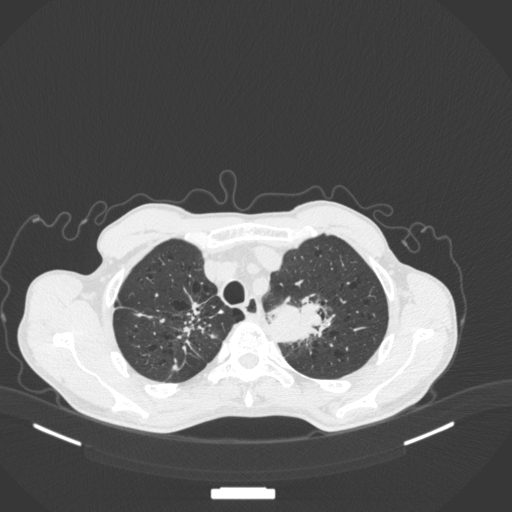
Chest CT, one axial slice; position 355 of 394 along the scan axis; 120 kVp; lung window (W 1500 / L -600 HU); 512 × 512 image matrix, field of view 400 × 400 mm. Patient: male, 65 years. Case-level facts recorded for this patient, not image findings: clinical TNM (as recorded): T2b N0 M0.
Structures marked on this image (rectangle marked by the reading radiologist):
- lung tumour (recorded histology: adenocarcinoma): box from (x=265, y=296) to (x=338, y=346) px